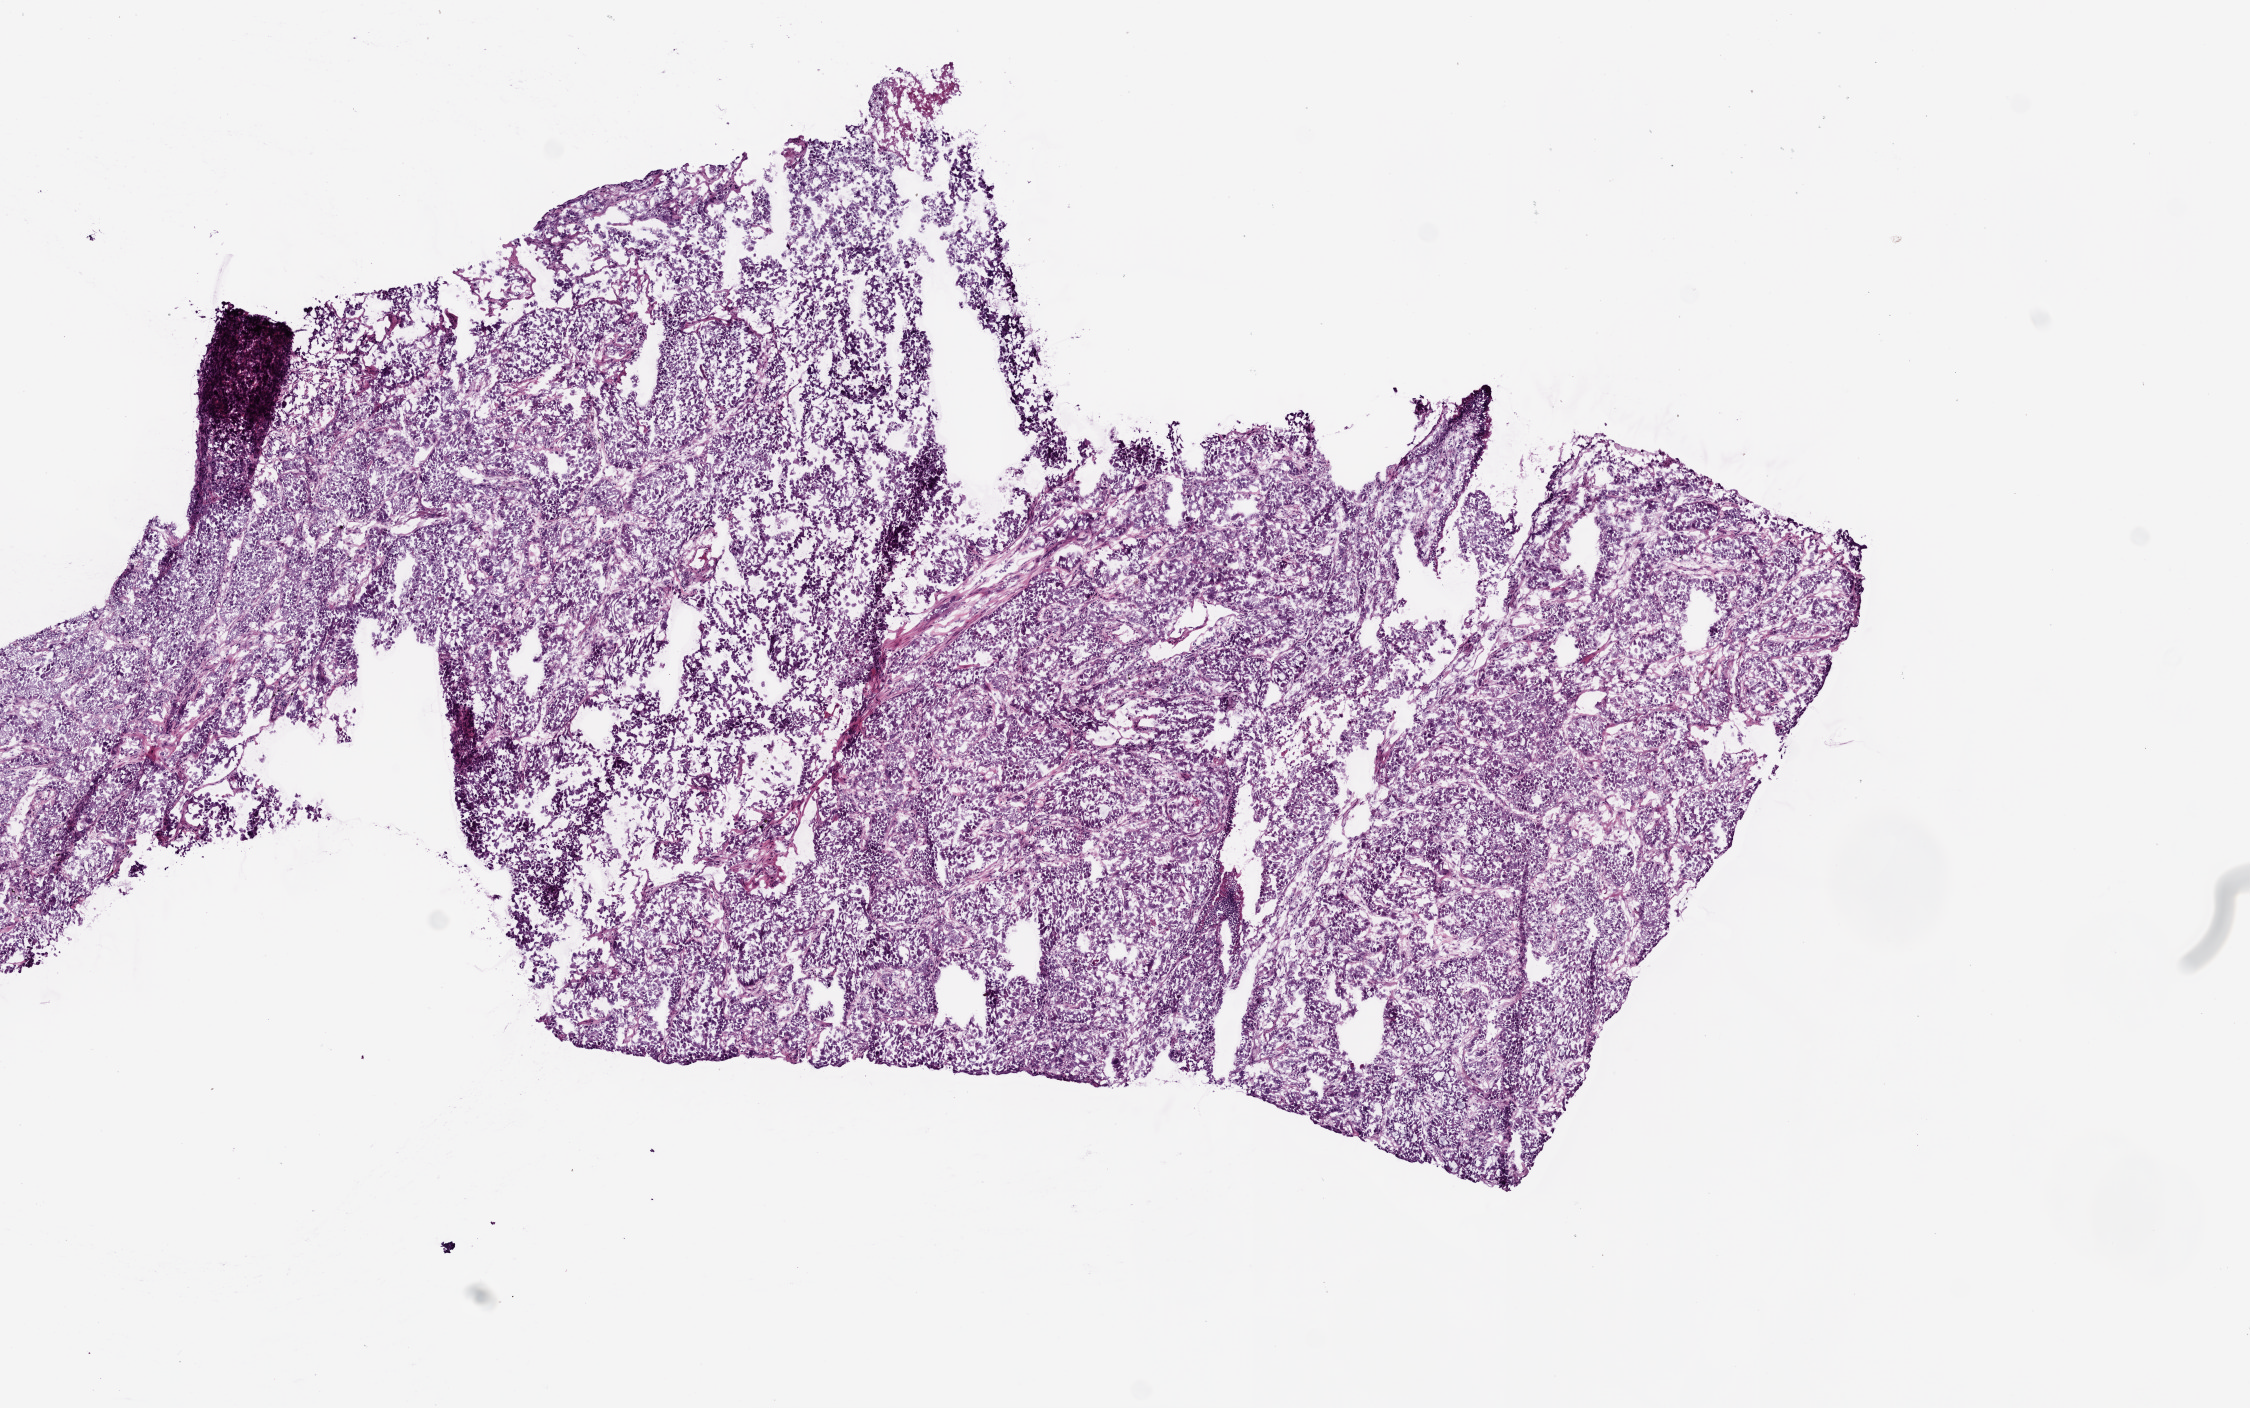
Digitized H&E-stained tissue section (whole slide), a low-resolution overview of the entire scanned area, about 9.0 x 5.6 mm (from a 20x scan). Frozen section from the bottom of the tissue portion. Sample: primary tumour, lung. Patient: male, age at initial diagnosis 76 years. Pathologist review of this section (percent, as recorded): tumour cells 95%, tumour nuclei 80%, normal cells 0%, stromal cells 5%, necrosis 0%.
* histologic diagnosis: Adenocarcinoma with mixed subtypes (upper lobe, lung)
* AJCC pathologic stage: IIIB (5th edition)
* laterality: left